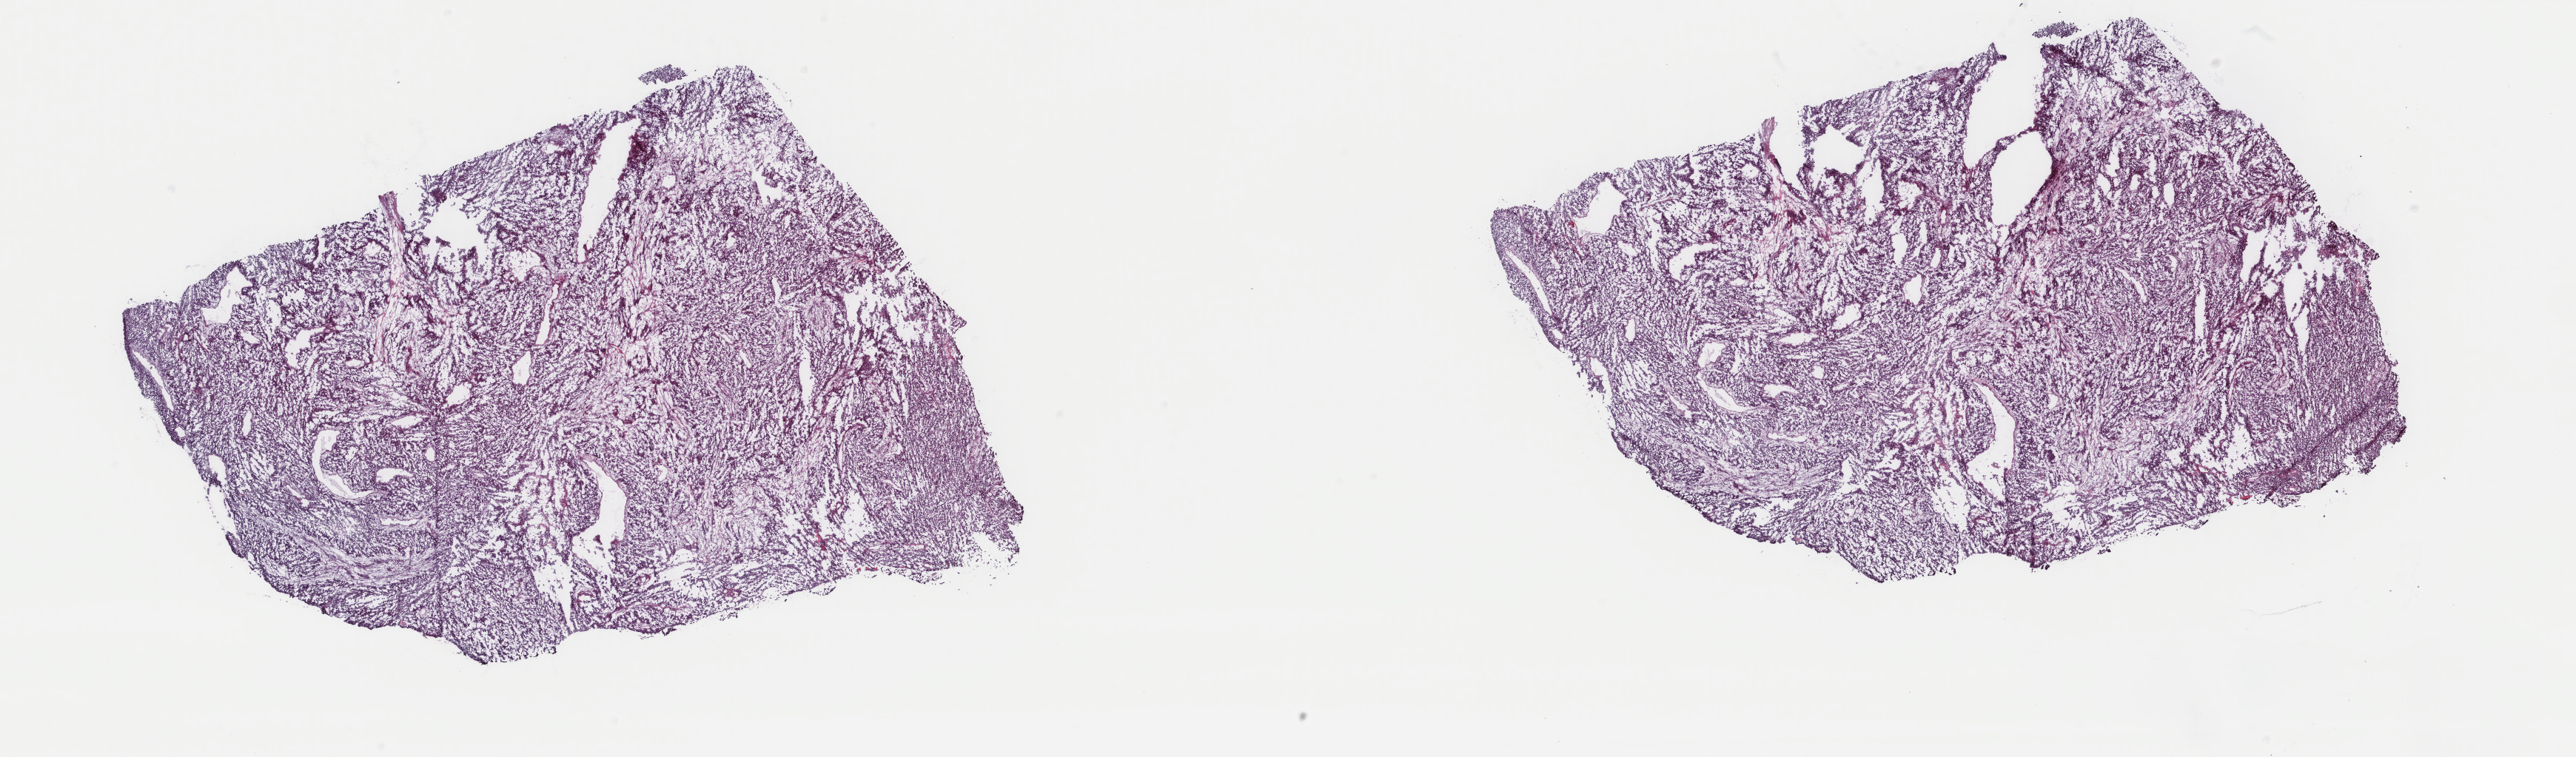
Whole-slide histology image, H&E, whole scanned area (about 27.6 x 8.1 mm, slide scanned at 40x) shown as a low-resolution overview; frozen section; metastatic tumour sample, sampled site not recorded. Patient: male, age at initial diagnosis 30 years. Pathologist review of this section (percent, as recorded): tumour cells 100%, tumour nuclei 80%.
This section: metastatic tumour tissue. Patient diagnosis: Malignant melanoma, NOS.